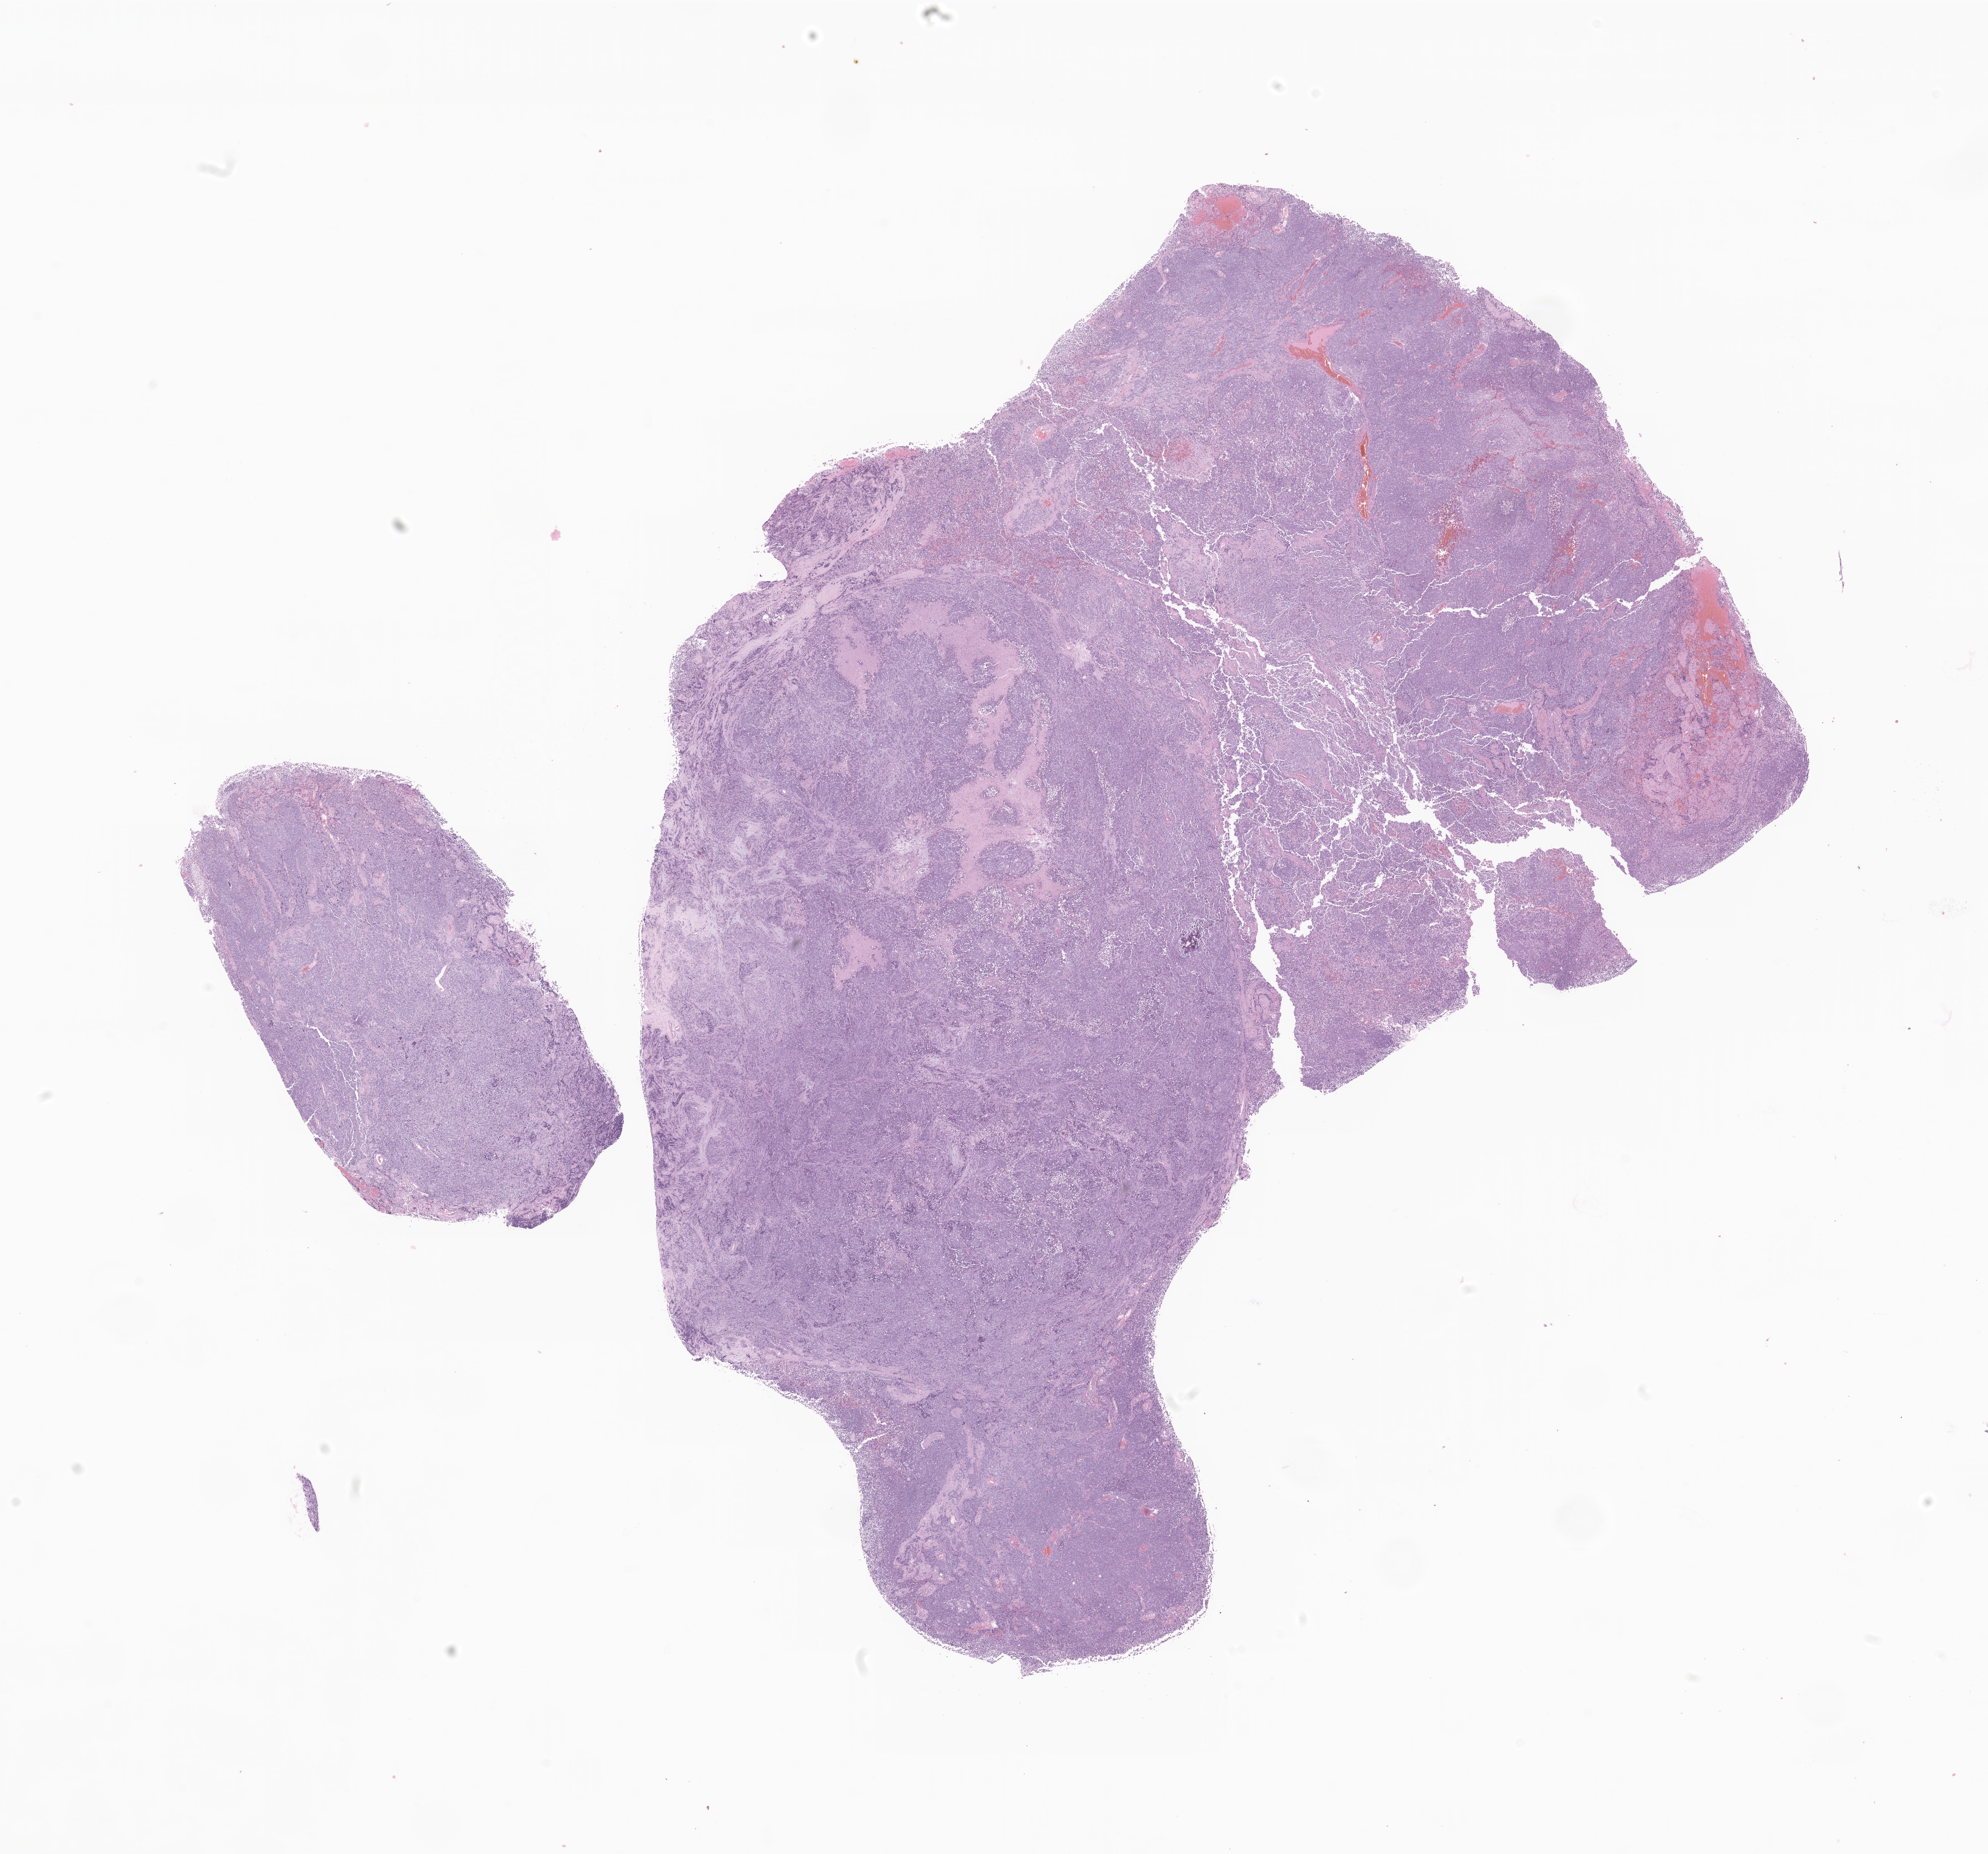
Whole-slide image, hematoxylin and eosin (H&E) stain of tumor tissue from the brain — low-resolution overview of the scanned area, about 20.6 x 19.2 mm; formalin-fixed, paraffin-embedded (FFPE) tissue. Patient: female, age 170 months.
Diagnosis (ICD-O-3 morphology term): Medulloblastoma, NOS.